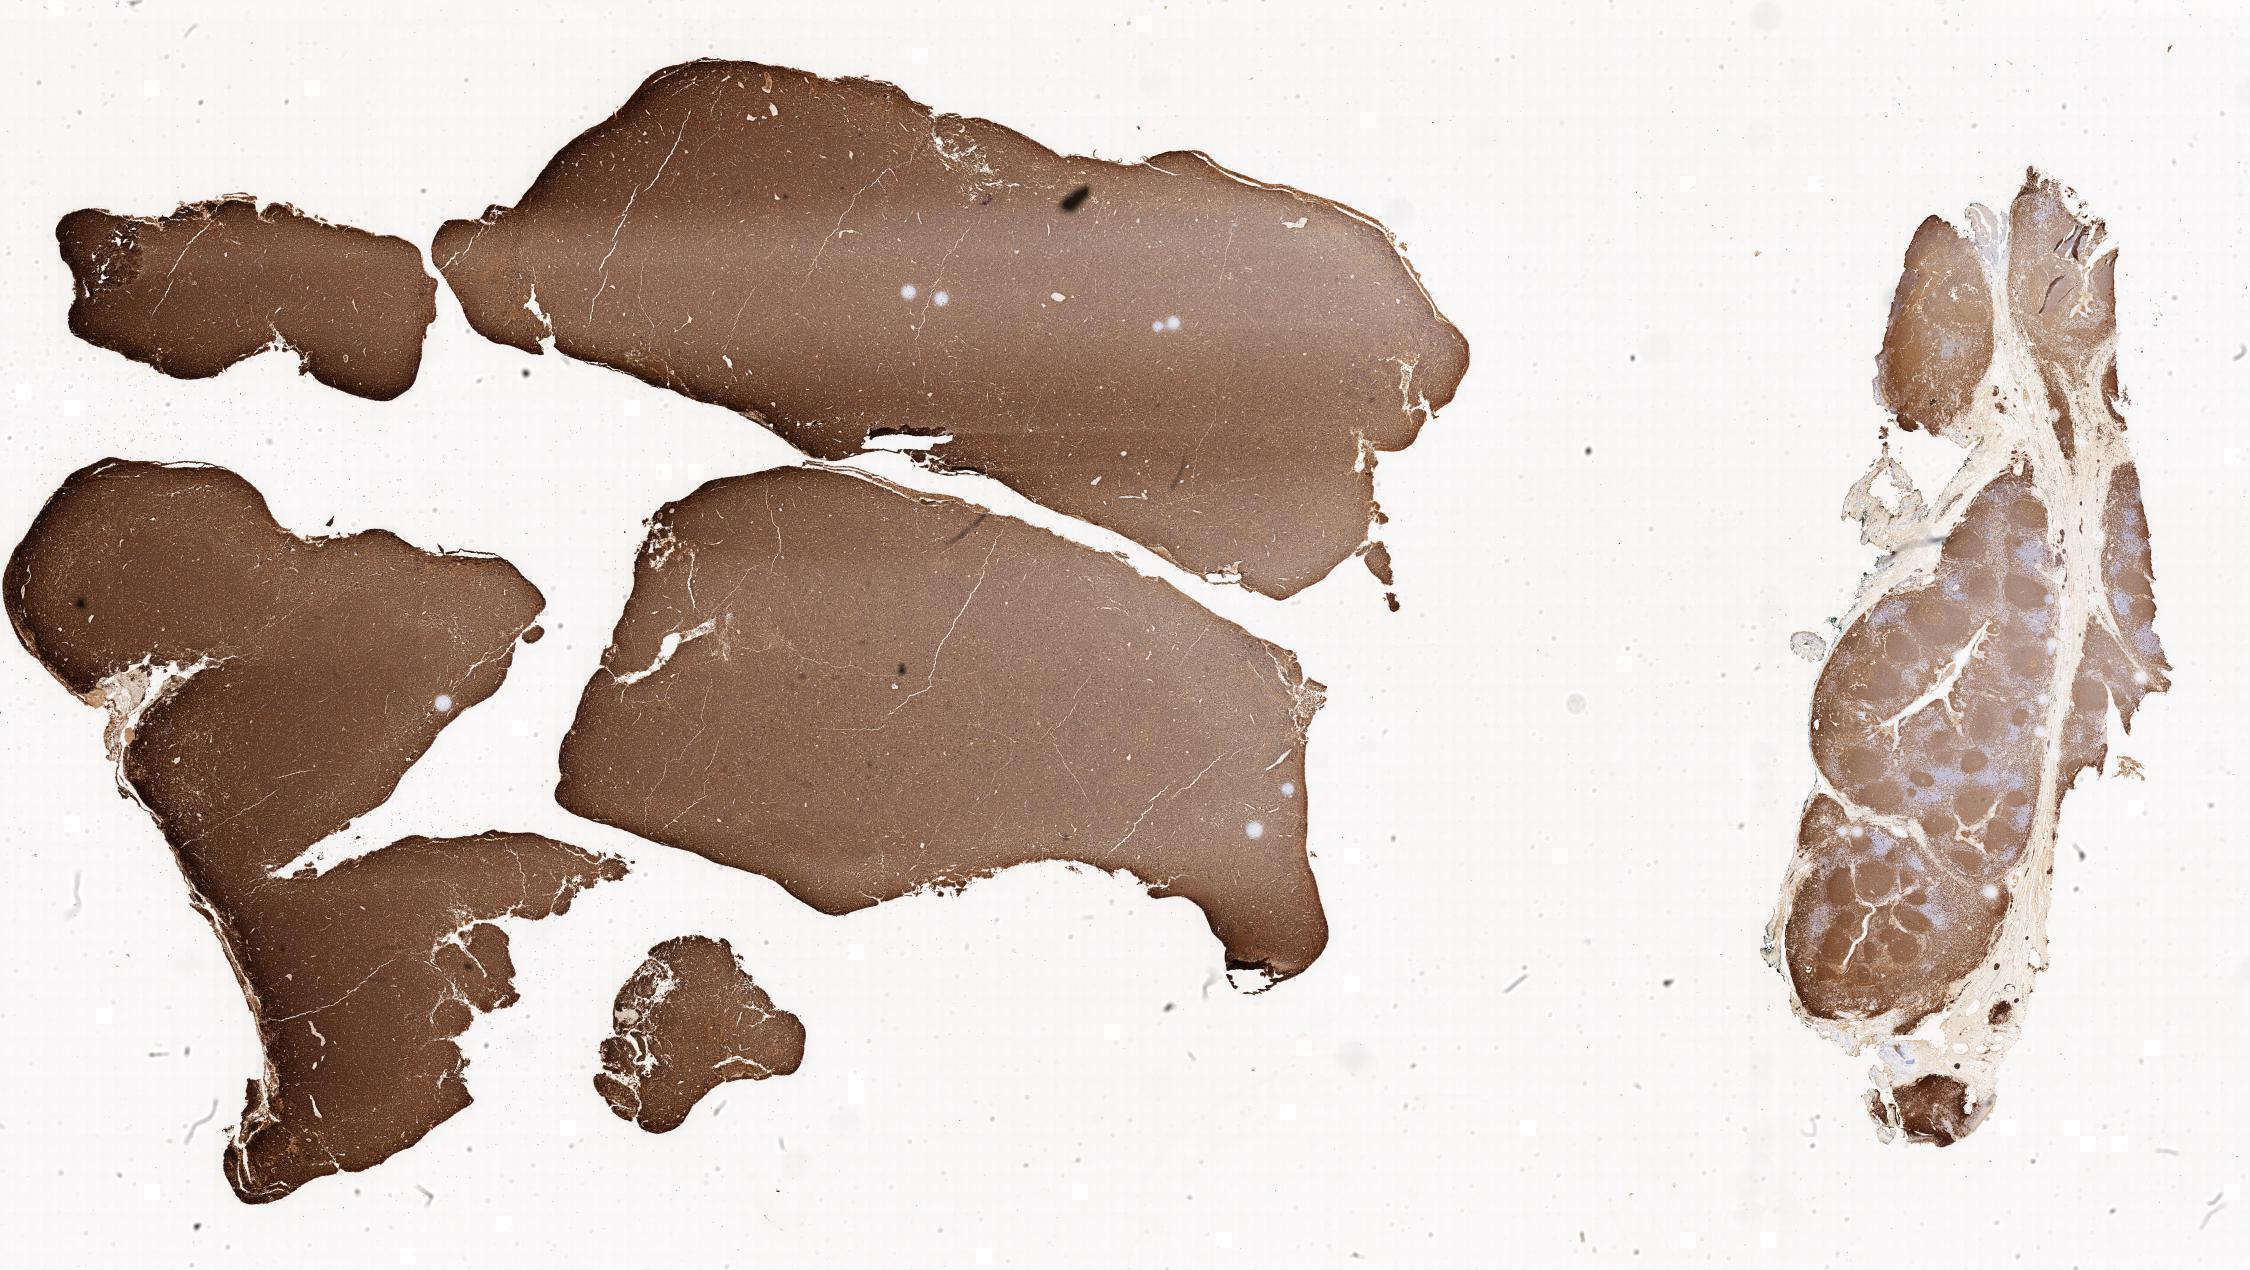
Immunohistochemistry (IHC) whole-slide image stained for CD20, a low-resolution overview of the entire scanned area. Tumor tissue. Anatomic site: peritoneum. Female, age 7 years at initial diagnosis.
Diagnosis: Burkitt lymphoma, NOS.